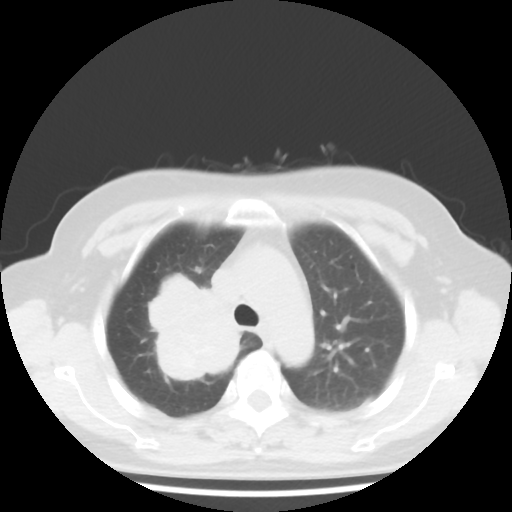
Chest CT, one axial slice; position 31 of 43 along the scan axis; reconstruction kernel STANDARD; 100 kVp; lung window (W 1500 / L -600 HU); 5 mm slice thickness; 512 × 512 image matrix, field of view 316 × 316 mm. Female patient, age 62 years. Case-level facts recorded for this patient, not image findings: clinical TNM (as recorded): T3 N0 M0.
Outlined on this slice (rectangle marked by the reading radiologist):
- lung tumour (recorded histology: small cell carcinoma): bounding box [x1, y1, x2, y2] px = [140, 267, 247, 383]